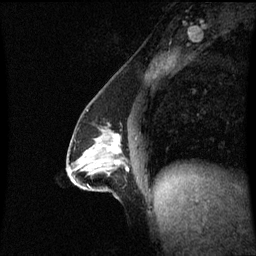
Breast MRI (dynamic contrast-enhanced), one sagittal slice; slice 31 of 60 in the series (ordered by position); dynamic contrast-enhanced series, image 2 of 3 at this slice position (ordered by acquisition); 1.5 T; TE 4.2 ms, TR 8.9 ms; 2.2 mm slice thickness; 256 × 256 image matrix, field of view 210 × 210 mm. Female patient, age 47 years. Case-level facts recorded for this patient, not image findings: setting: breast cancer imaged before/during neoadjuvant chemotherapy; receptor status: HR-positive, HER2-negative.
Annotated regions visible in this slice (semi-automatic segmentation, software-assisted and operator-edited):
- analysis volume of interest (the breast-tissue region the enhancement analysis was run in; not a lesion): bounding box <69,127,131,196> (left, top, right, bottom; pixels)
- tumour enhancement mask (voxels above the 70 % enhancement threshold inside the analysis volume of interest): <109,135,120,154>